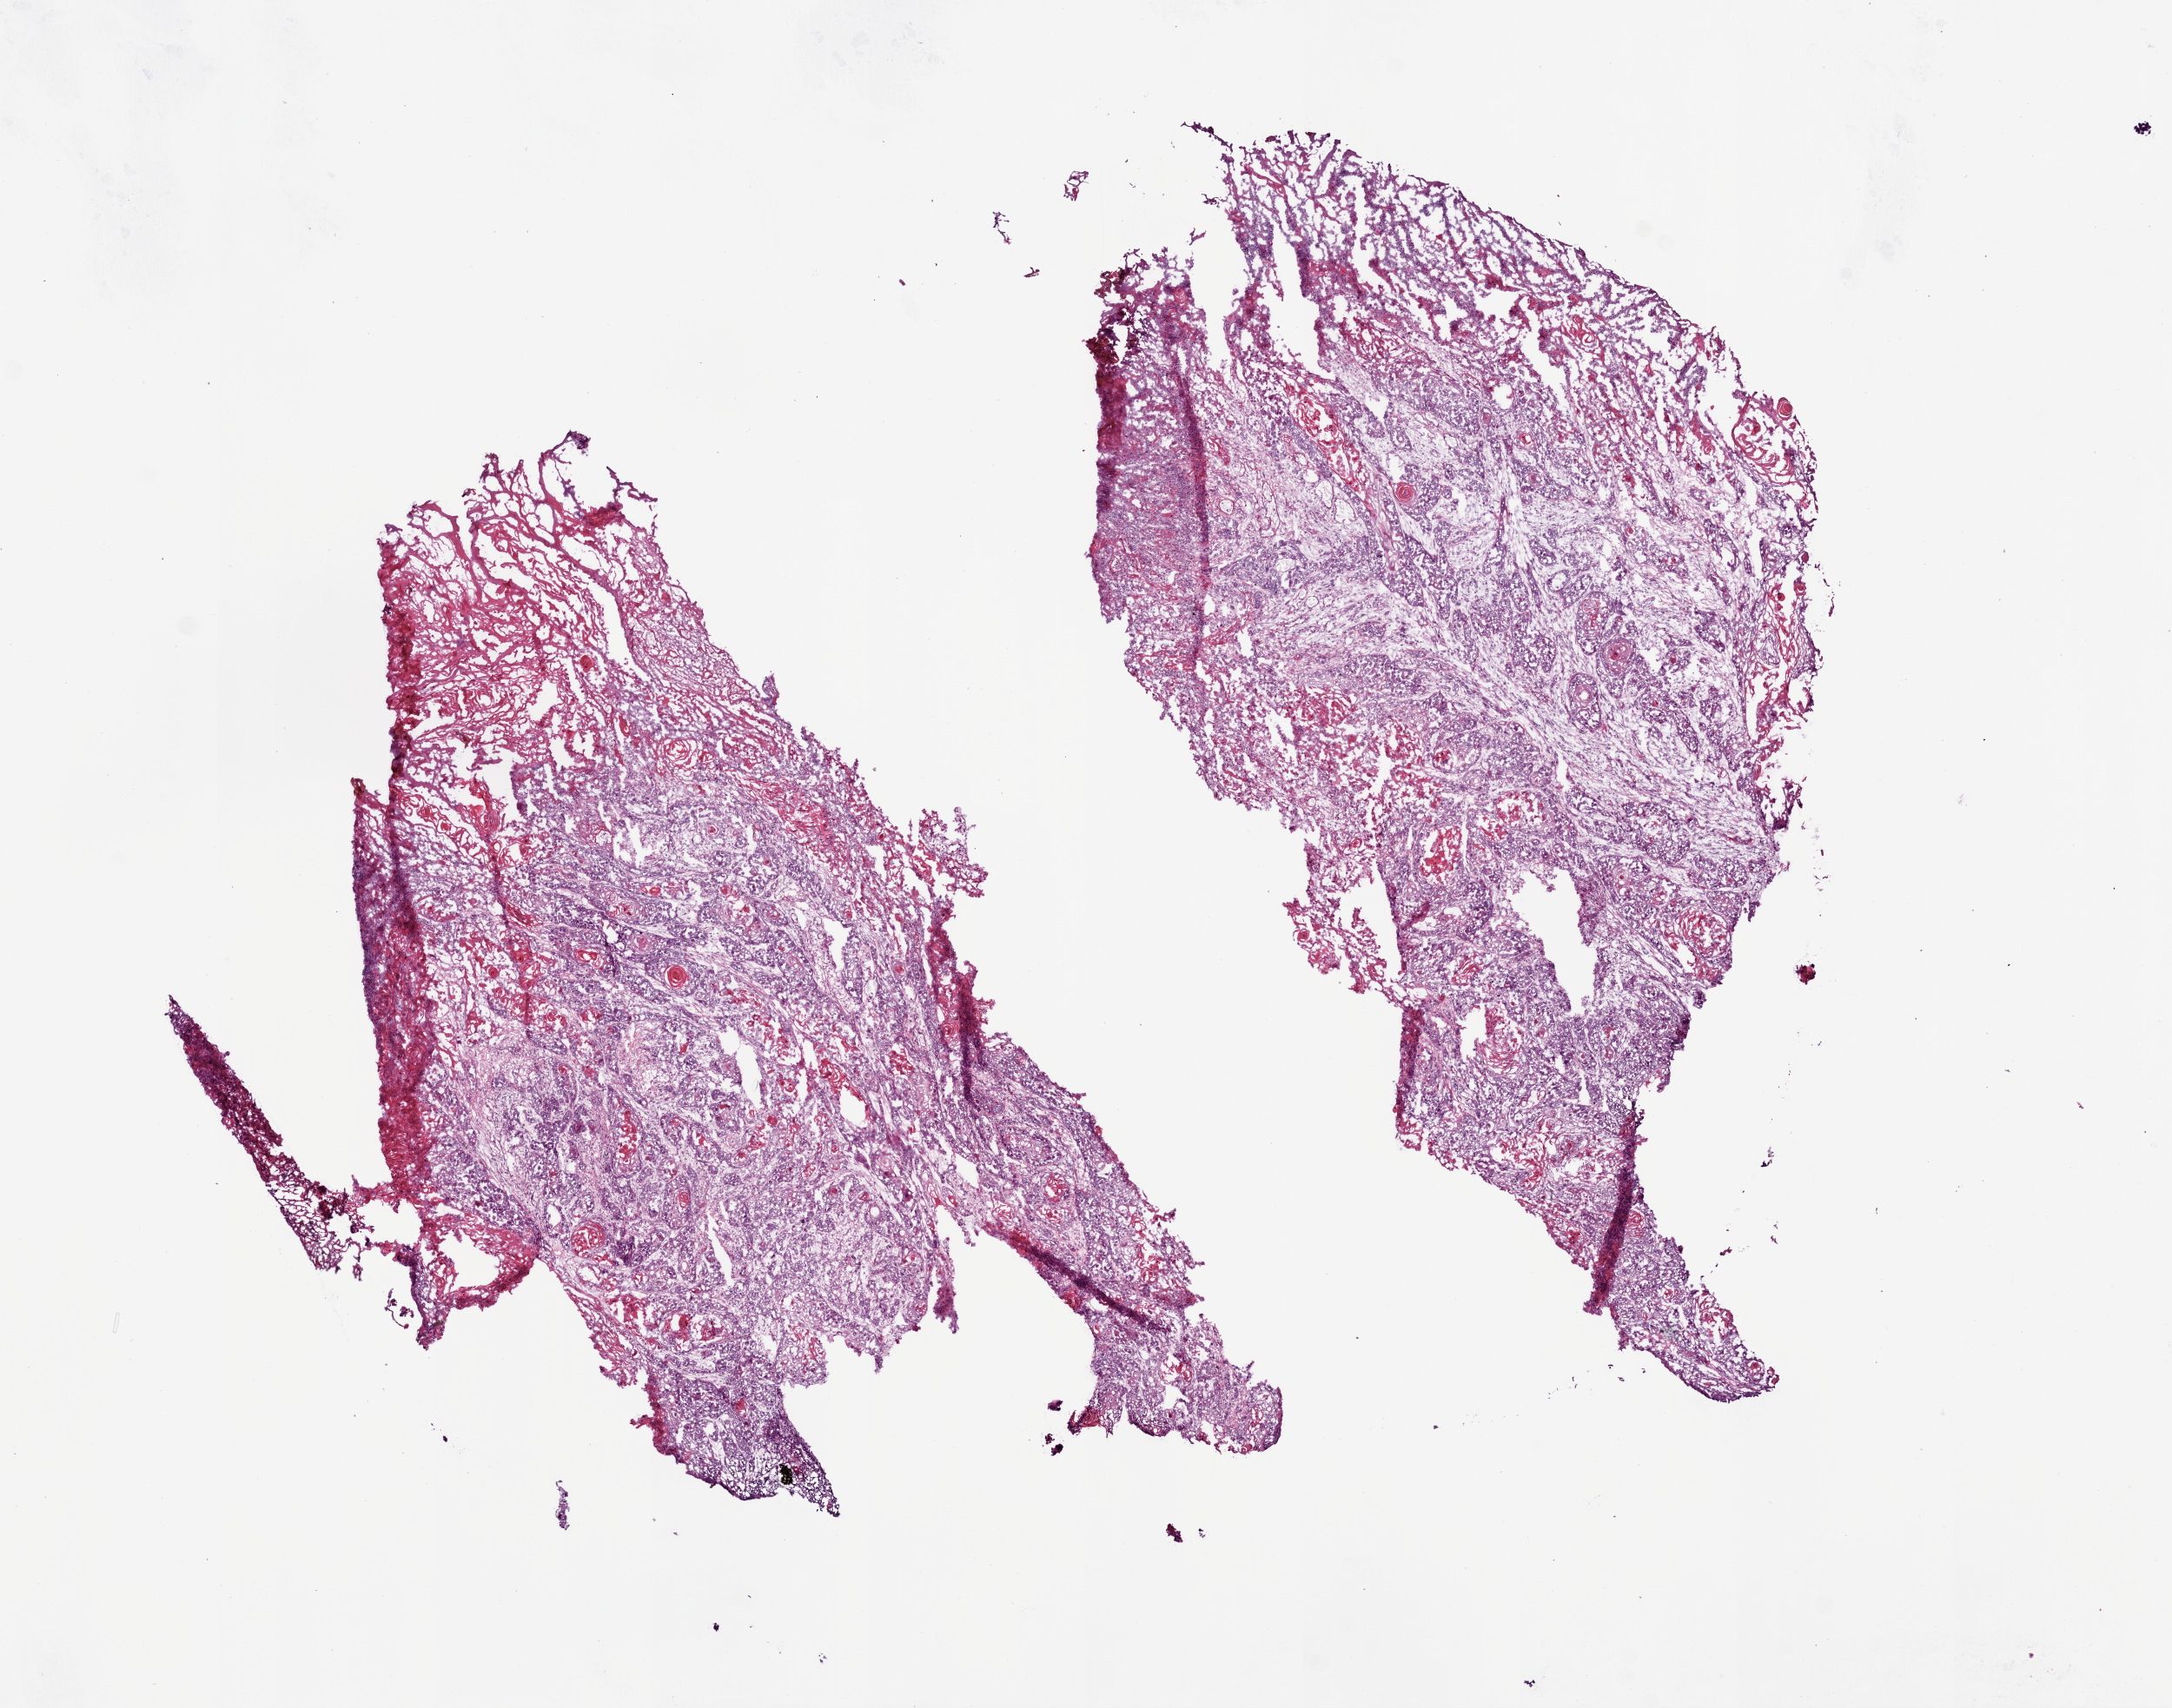
H&E whole-slide image — whole scanned area (about 10.0 x 7.9 mm, slide scanned at 20x) shown as a low-resolution overview, frozen section, primary tumour sample from the head and neck. Patient: male, age at initial diagnosis 67 years.
Histologic diagnosis: Squamous cell carcinoma, NOS (overlapping lesion of lip, oral cavity and pharynx).